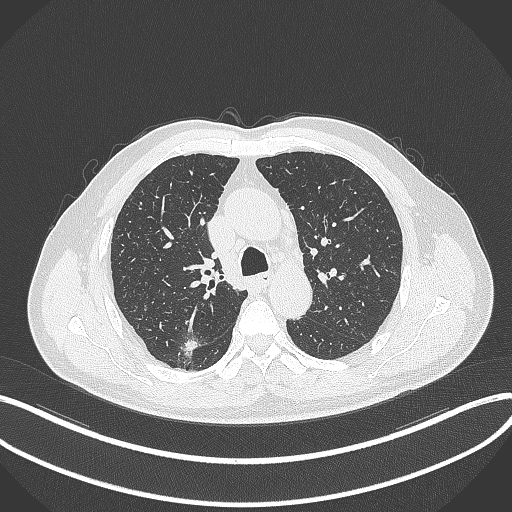
Chest CT, one axial slice. Reconstruction kernel B70f. 120 kVp. Lung window (W 1500 / L -600 HU). 1 mm slice thickness. 512 × 512 image matrix. Patient: male, 69 years. From the clinical record (not read from this slice): clinical TNM (as recorded): T1b N0 M0.
Annotated regions visible in this slice (rectangle marked by the reading radiologist):
- lung tumour (recorded histology: adenocarcinoma): bounding box [x1, y1, x2, y2] px = [179, 339, 199, 358]